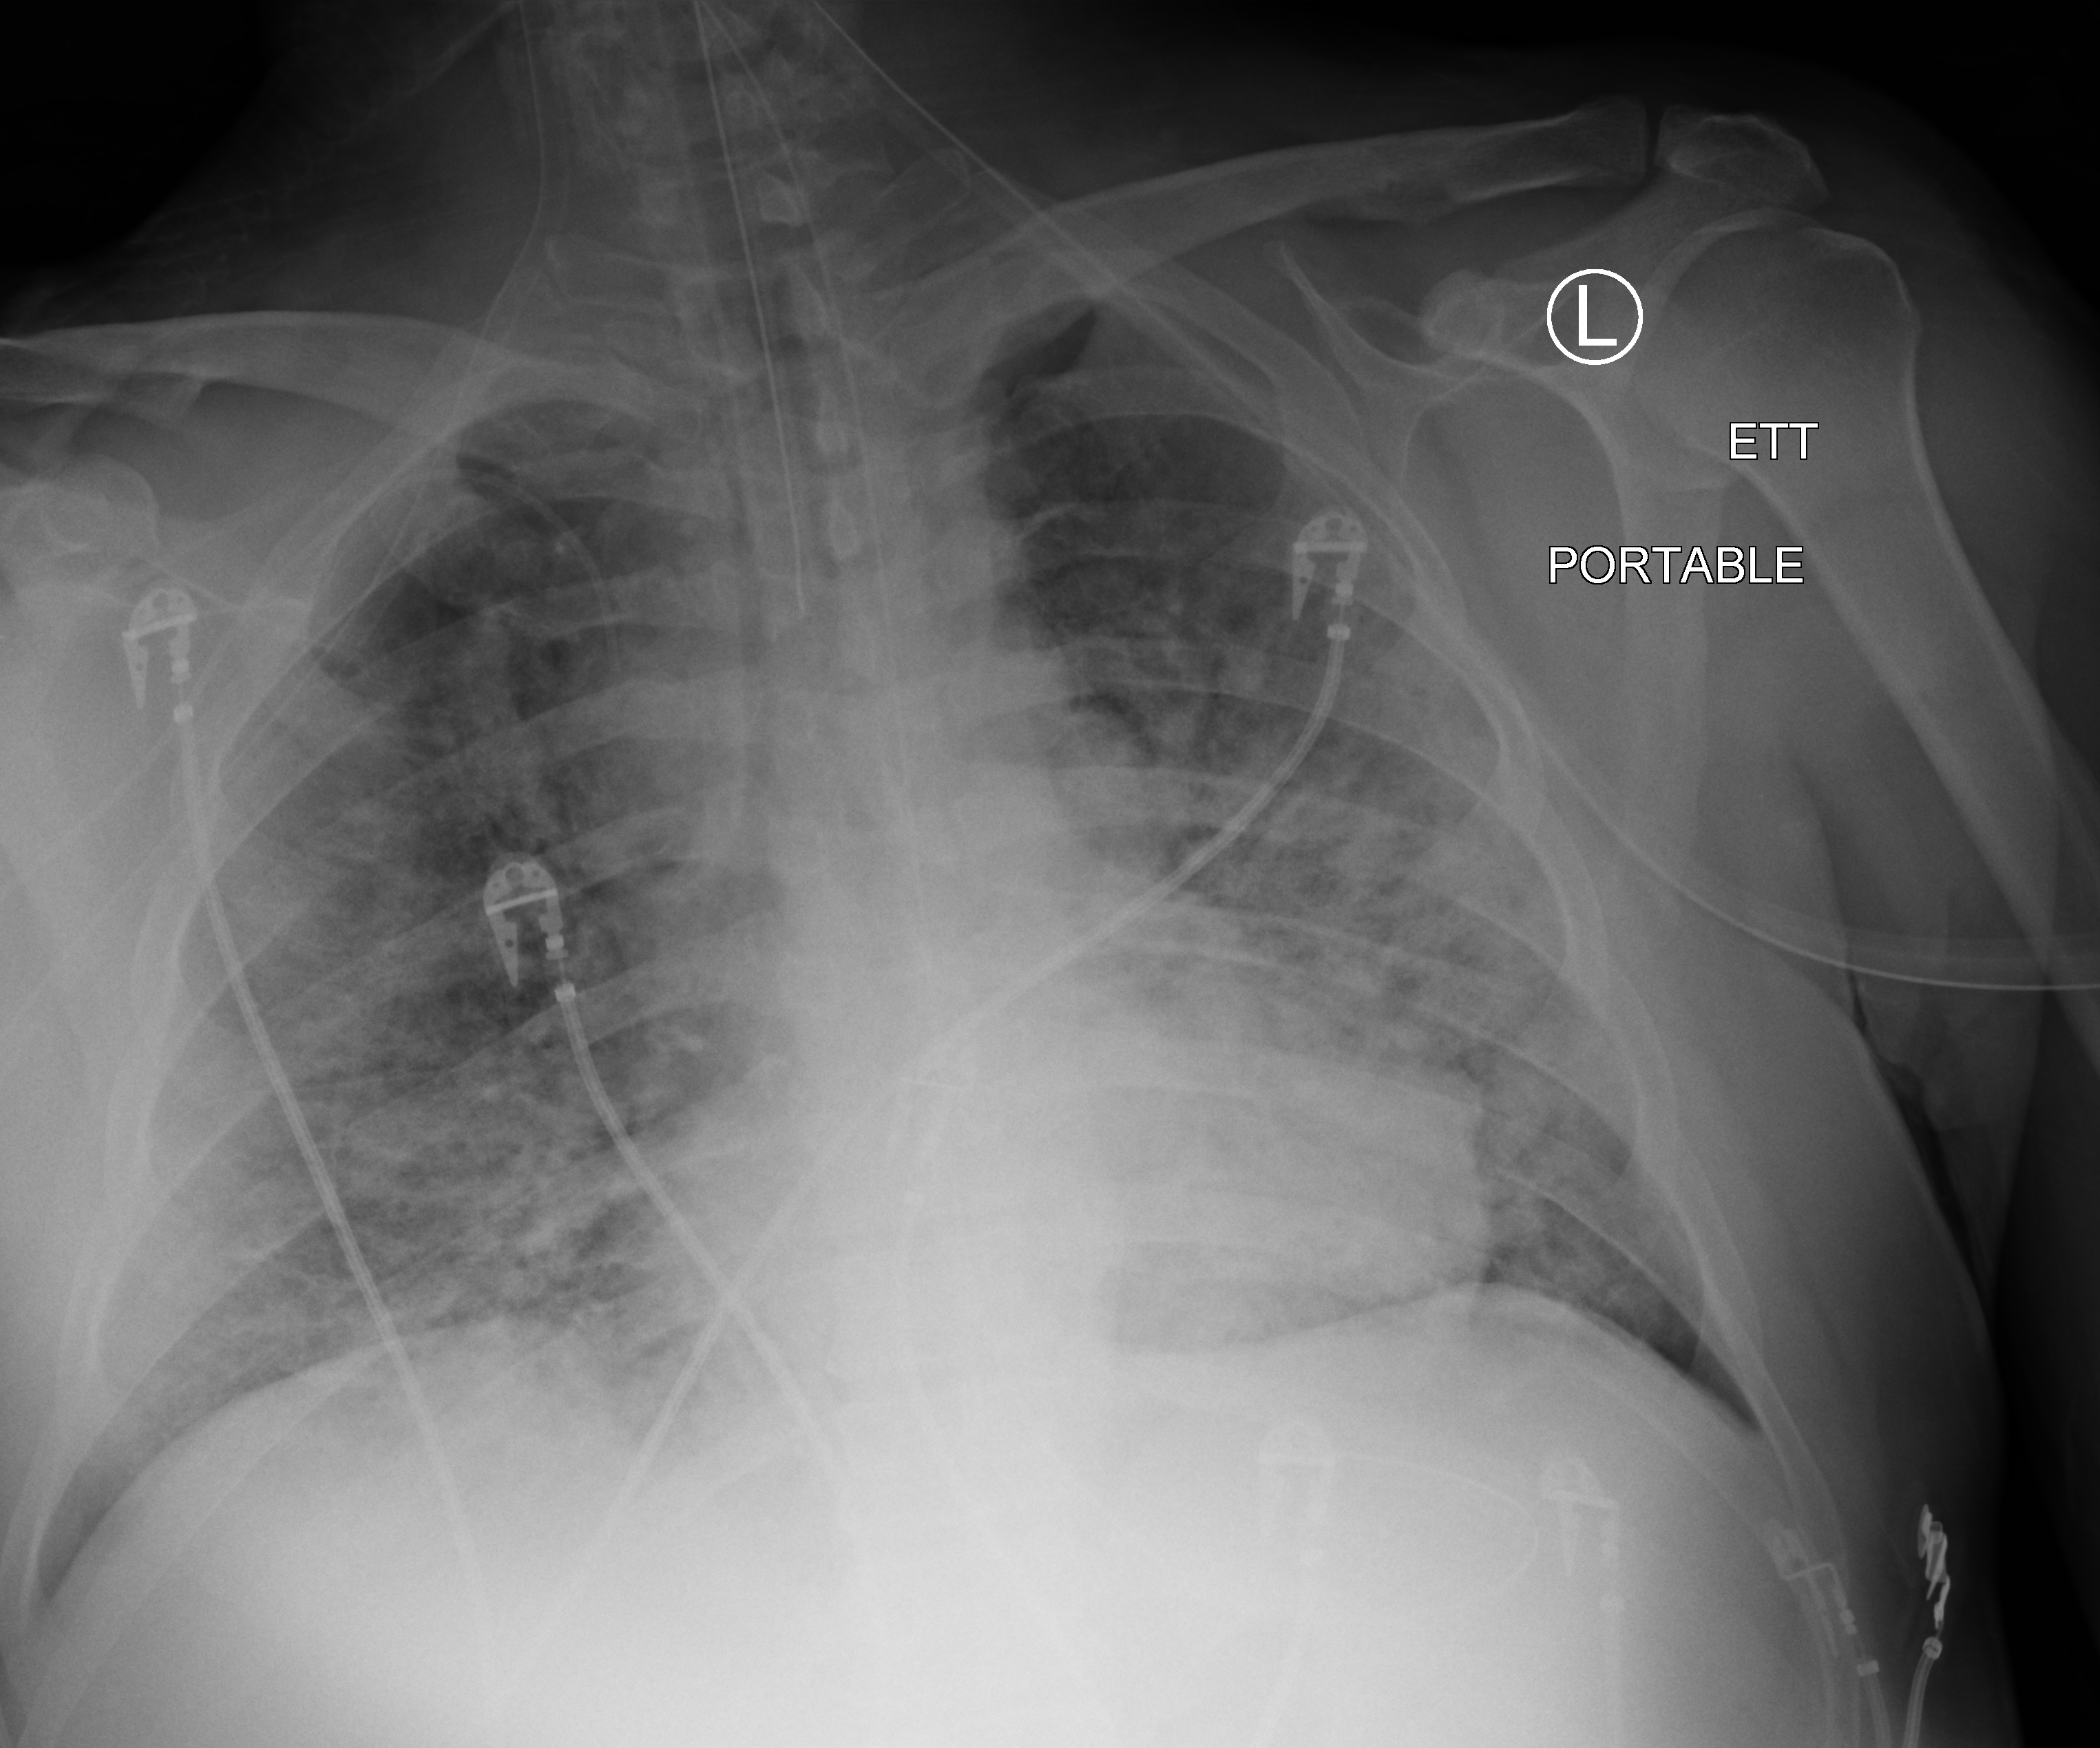
Chest X-ray (portable), anteroposterior (AP) projection. Male patient hospitalised with COVID-19, age 18–59 years.
Admission-level facts for this patient (not findings on this image; timing relative to this image not recorded): COPD (admission record): no; admitted to intensive care during this hospital stay: yes; mechanically ventilated during this hospital stay: yes.